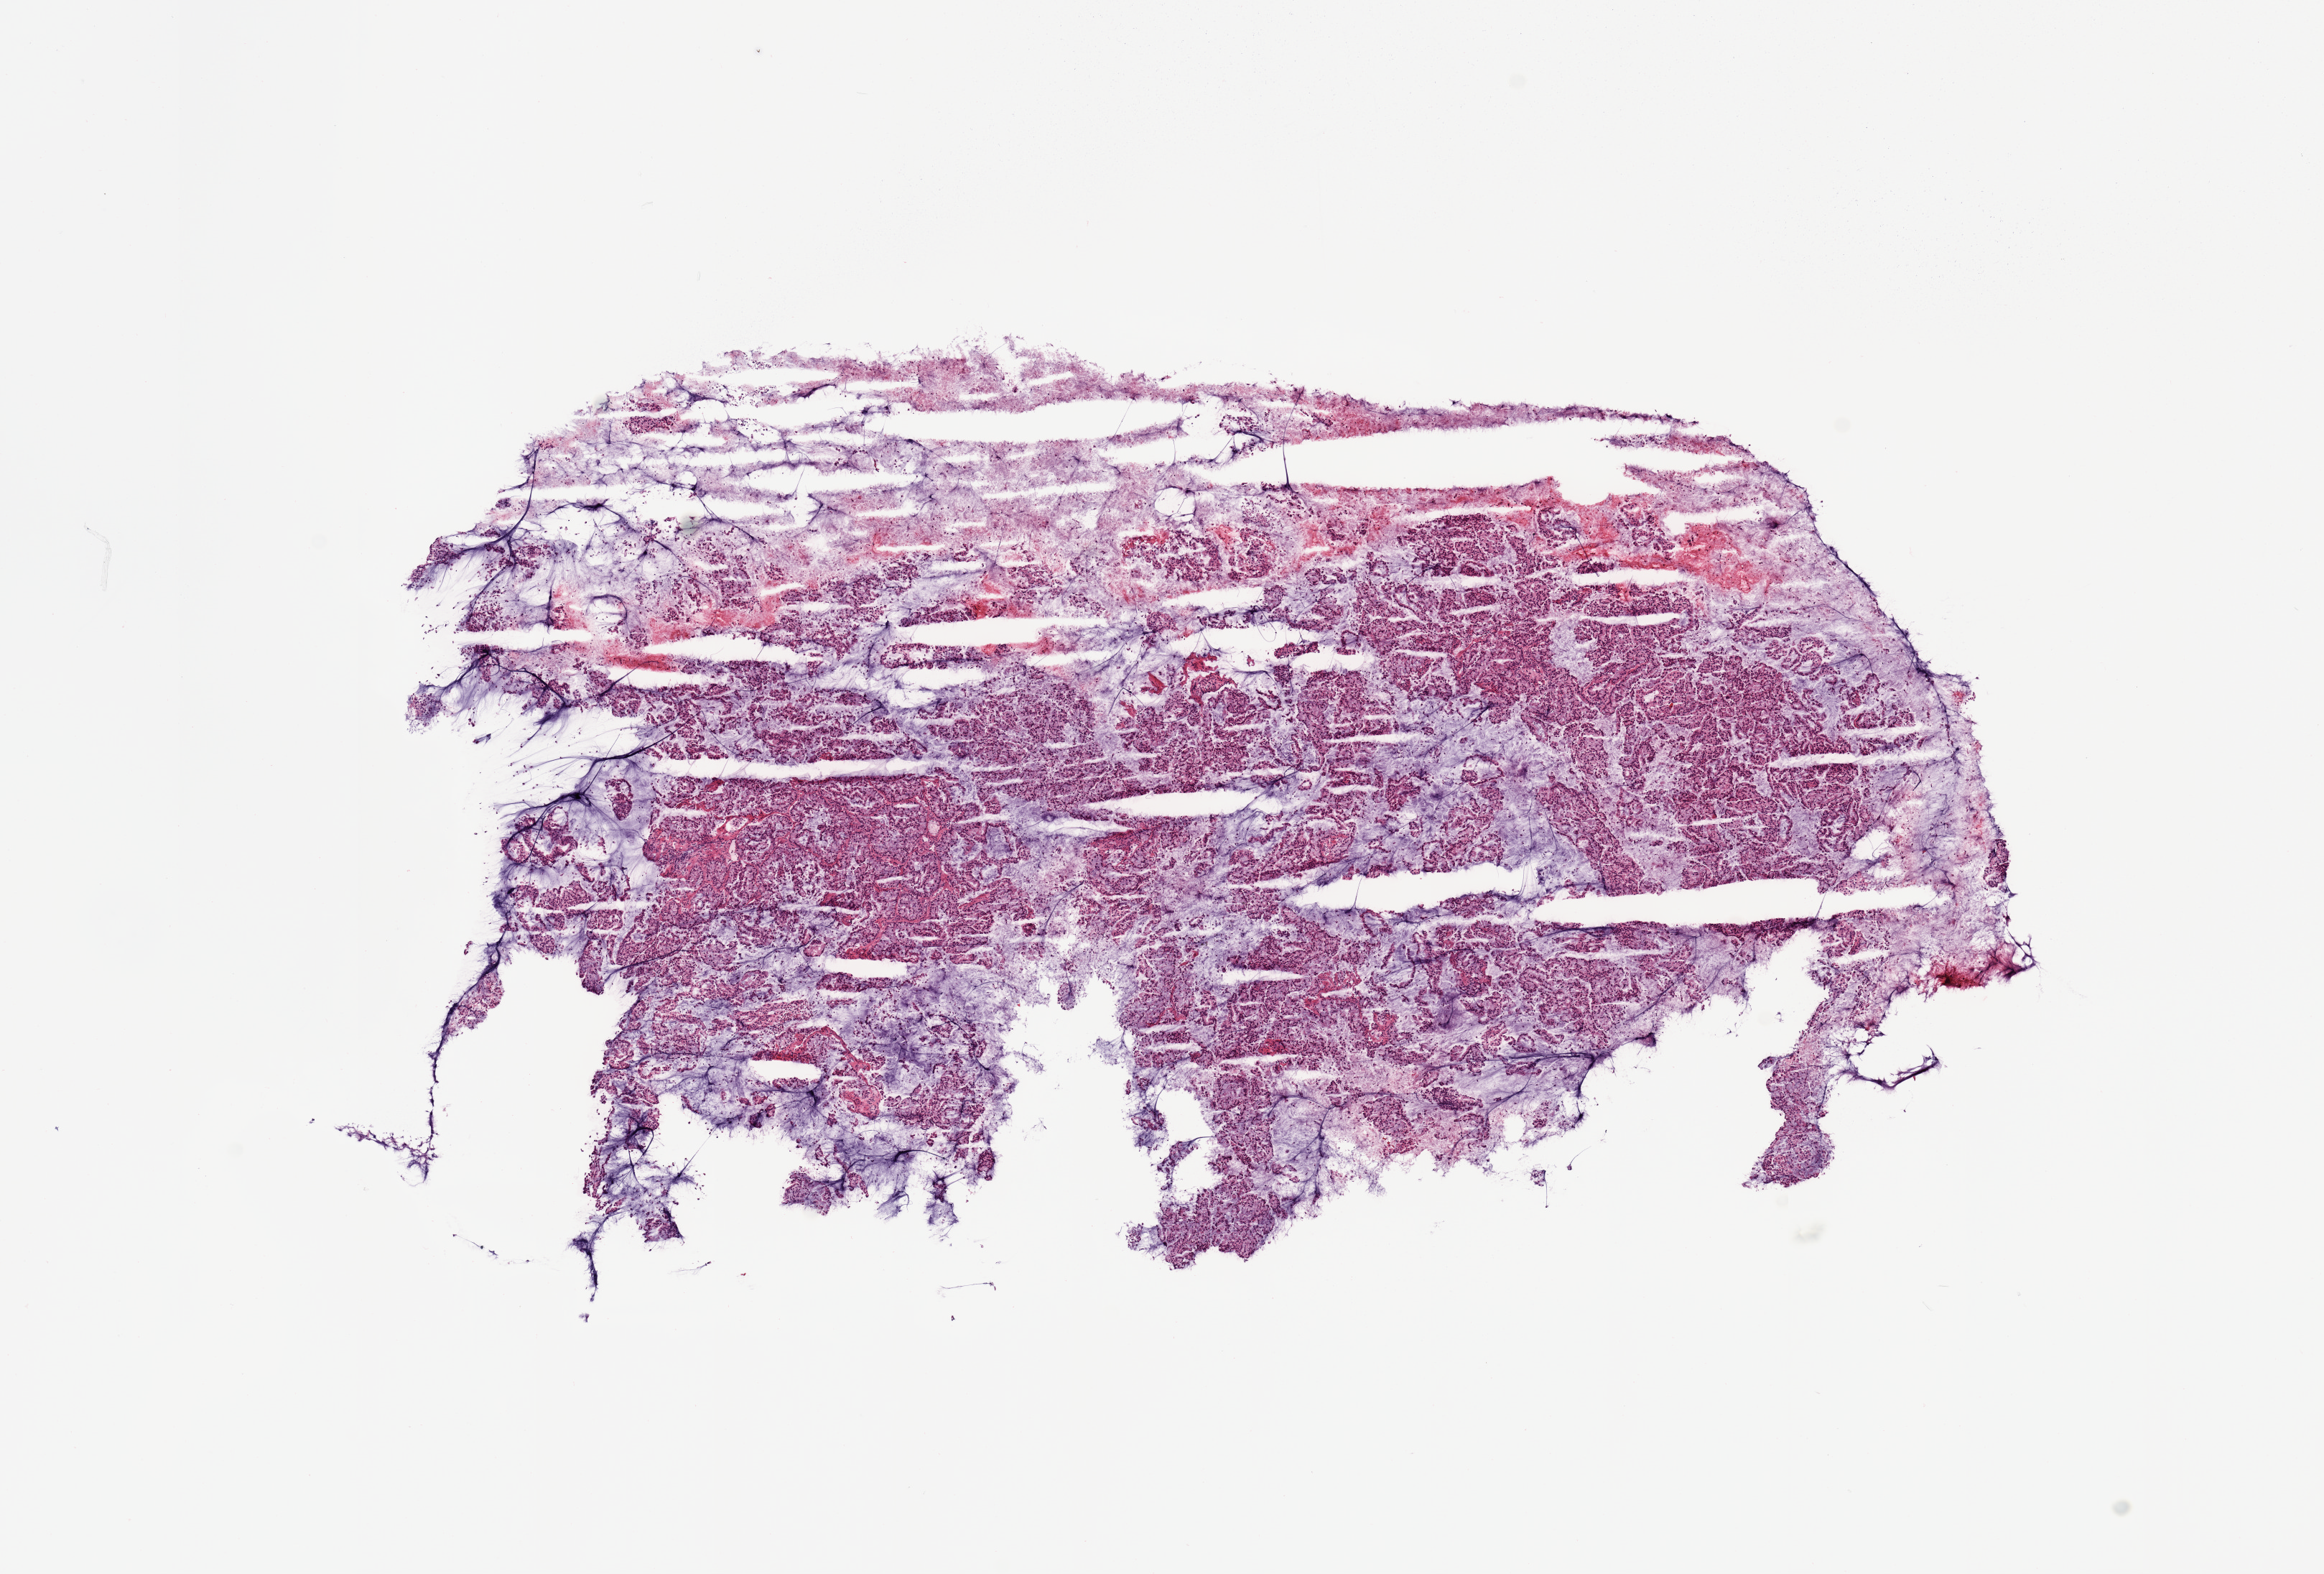
Hematoxylin and eosin (H&E) stained whole-slide image, whole scanned area (about 12.8 x 8.7 mm) shown as a low-resolution overview, tumour tissue sample, sampled site: lung. 35-year-old female patient. Histologic grade: G3 (poorly differentiated). Pathologist review of this section (percent, as recorded): tumour nuclei 85%, necrosis 5%.
Primary tumour site (as recorded): left lower lobe. Diagnosis: Adenocarcinoma, NOS. AJCC pathologic stage: IB.